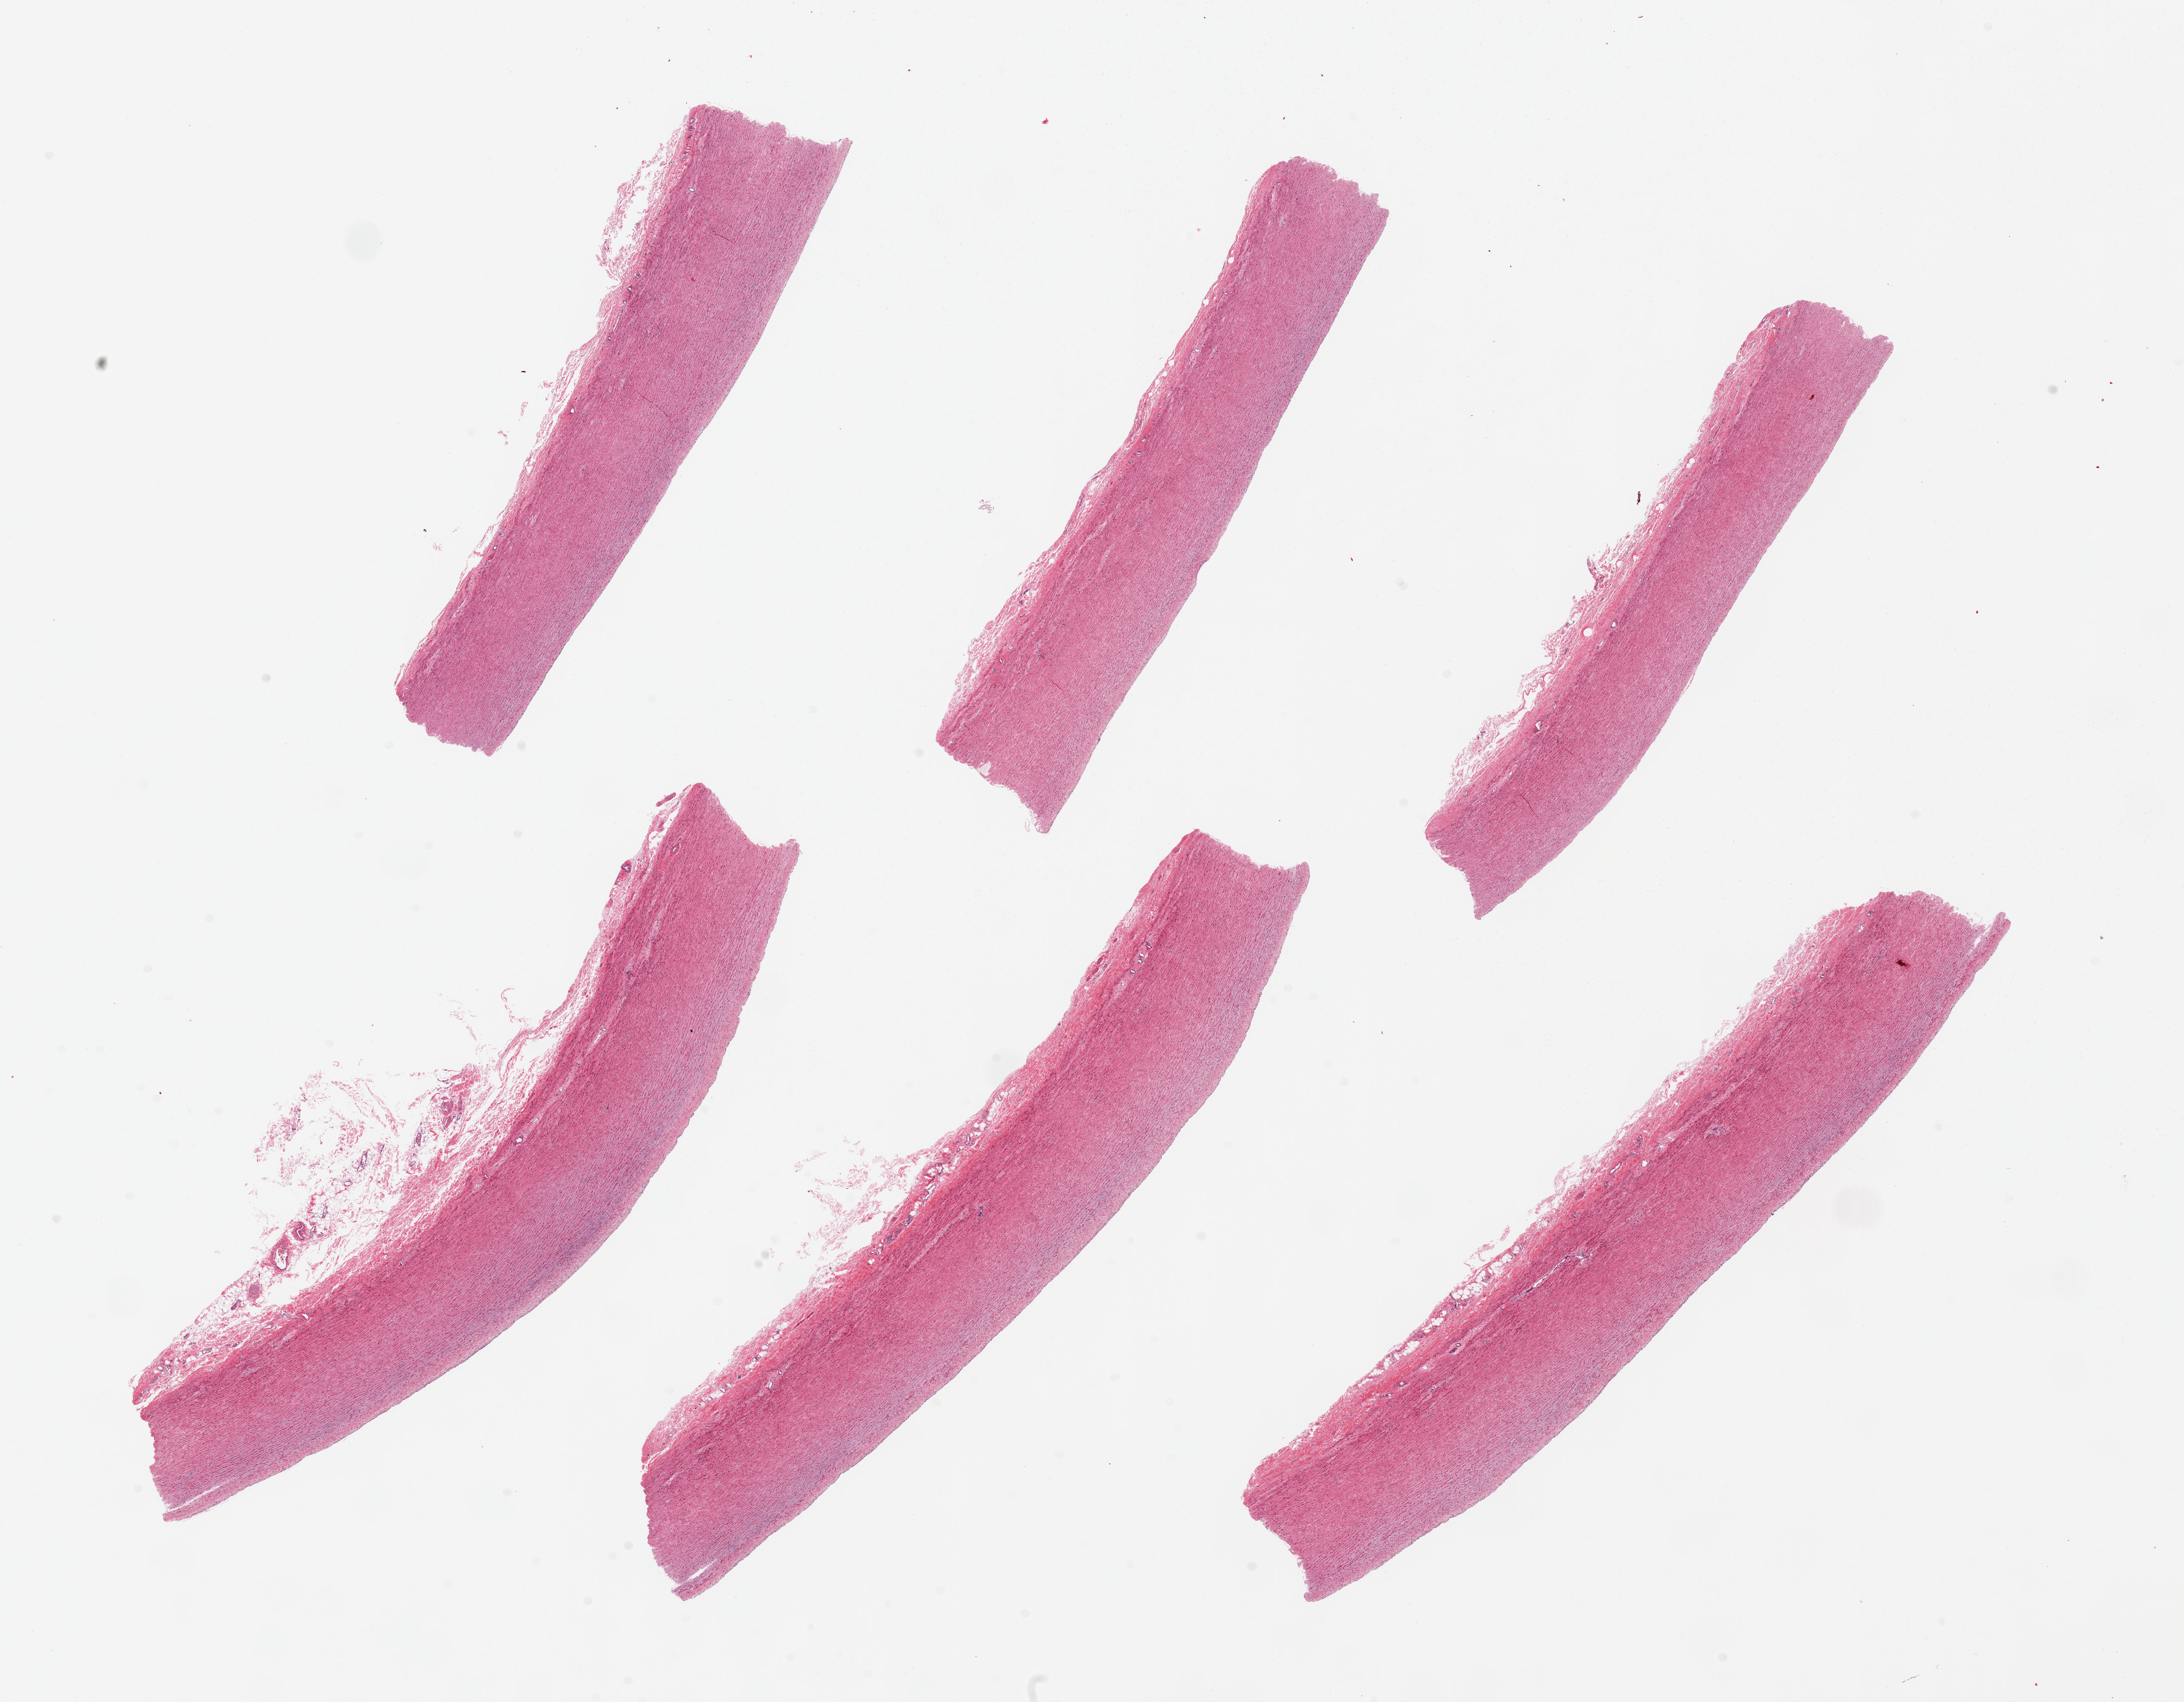
Whole-slide image, haematoxylin and eosin stain, a low-resolution overview of the entire scanned area, about 26.6 x 20.7 mm (acquisition: 20x scan); PAXgene-fixed paraffin-embedded (PFPE) section; section of aorta (target tissue); donor tissue sample. Male donor.
• reviewer comment on this tissue sample: 6 pieces ~10x1.5mm